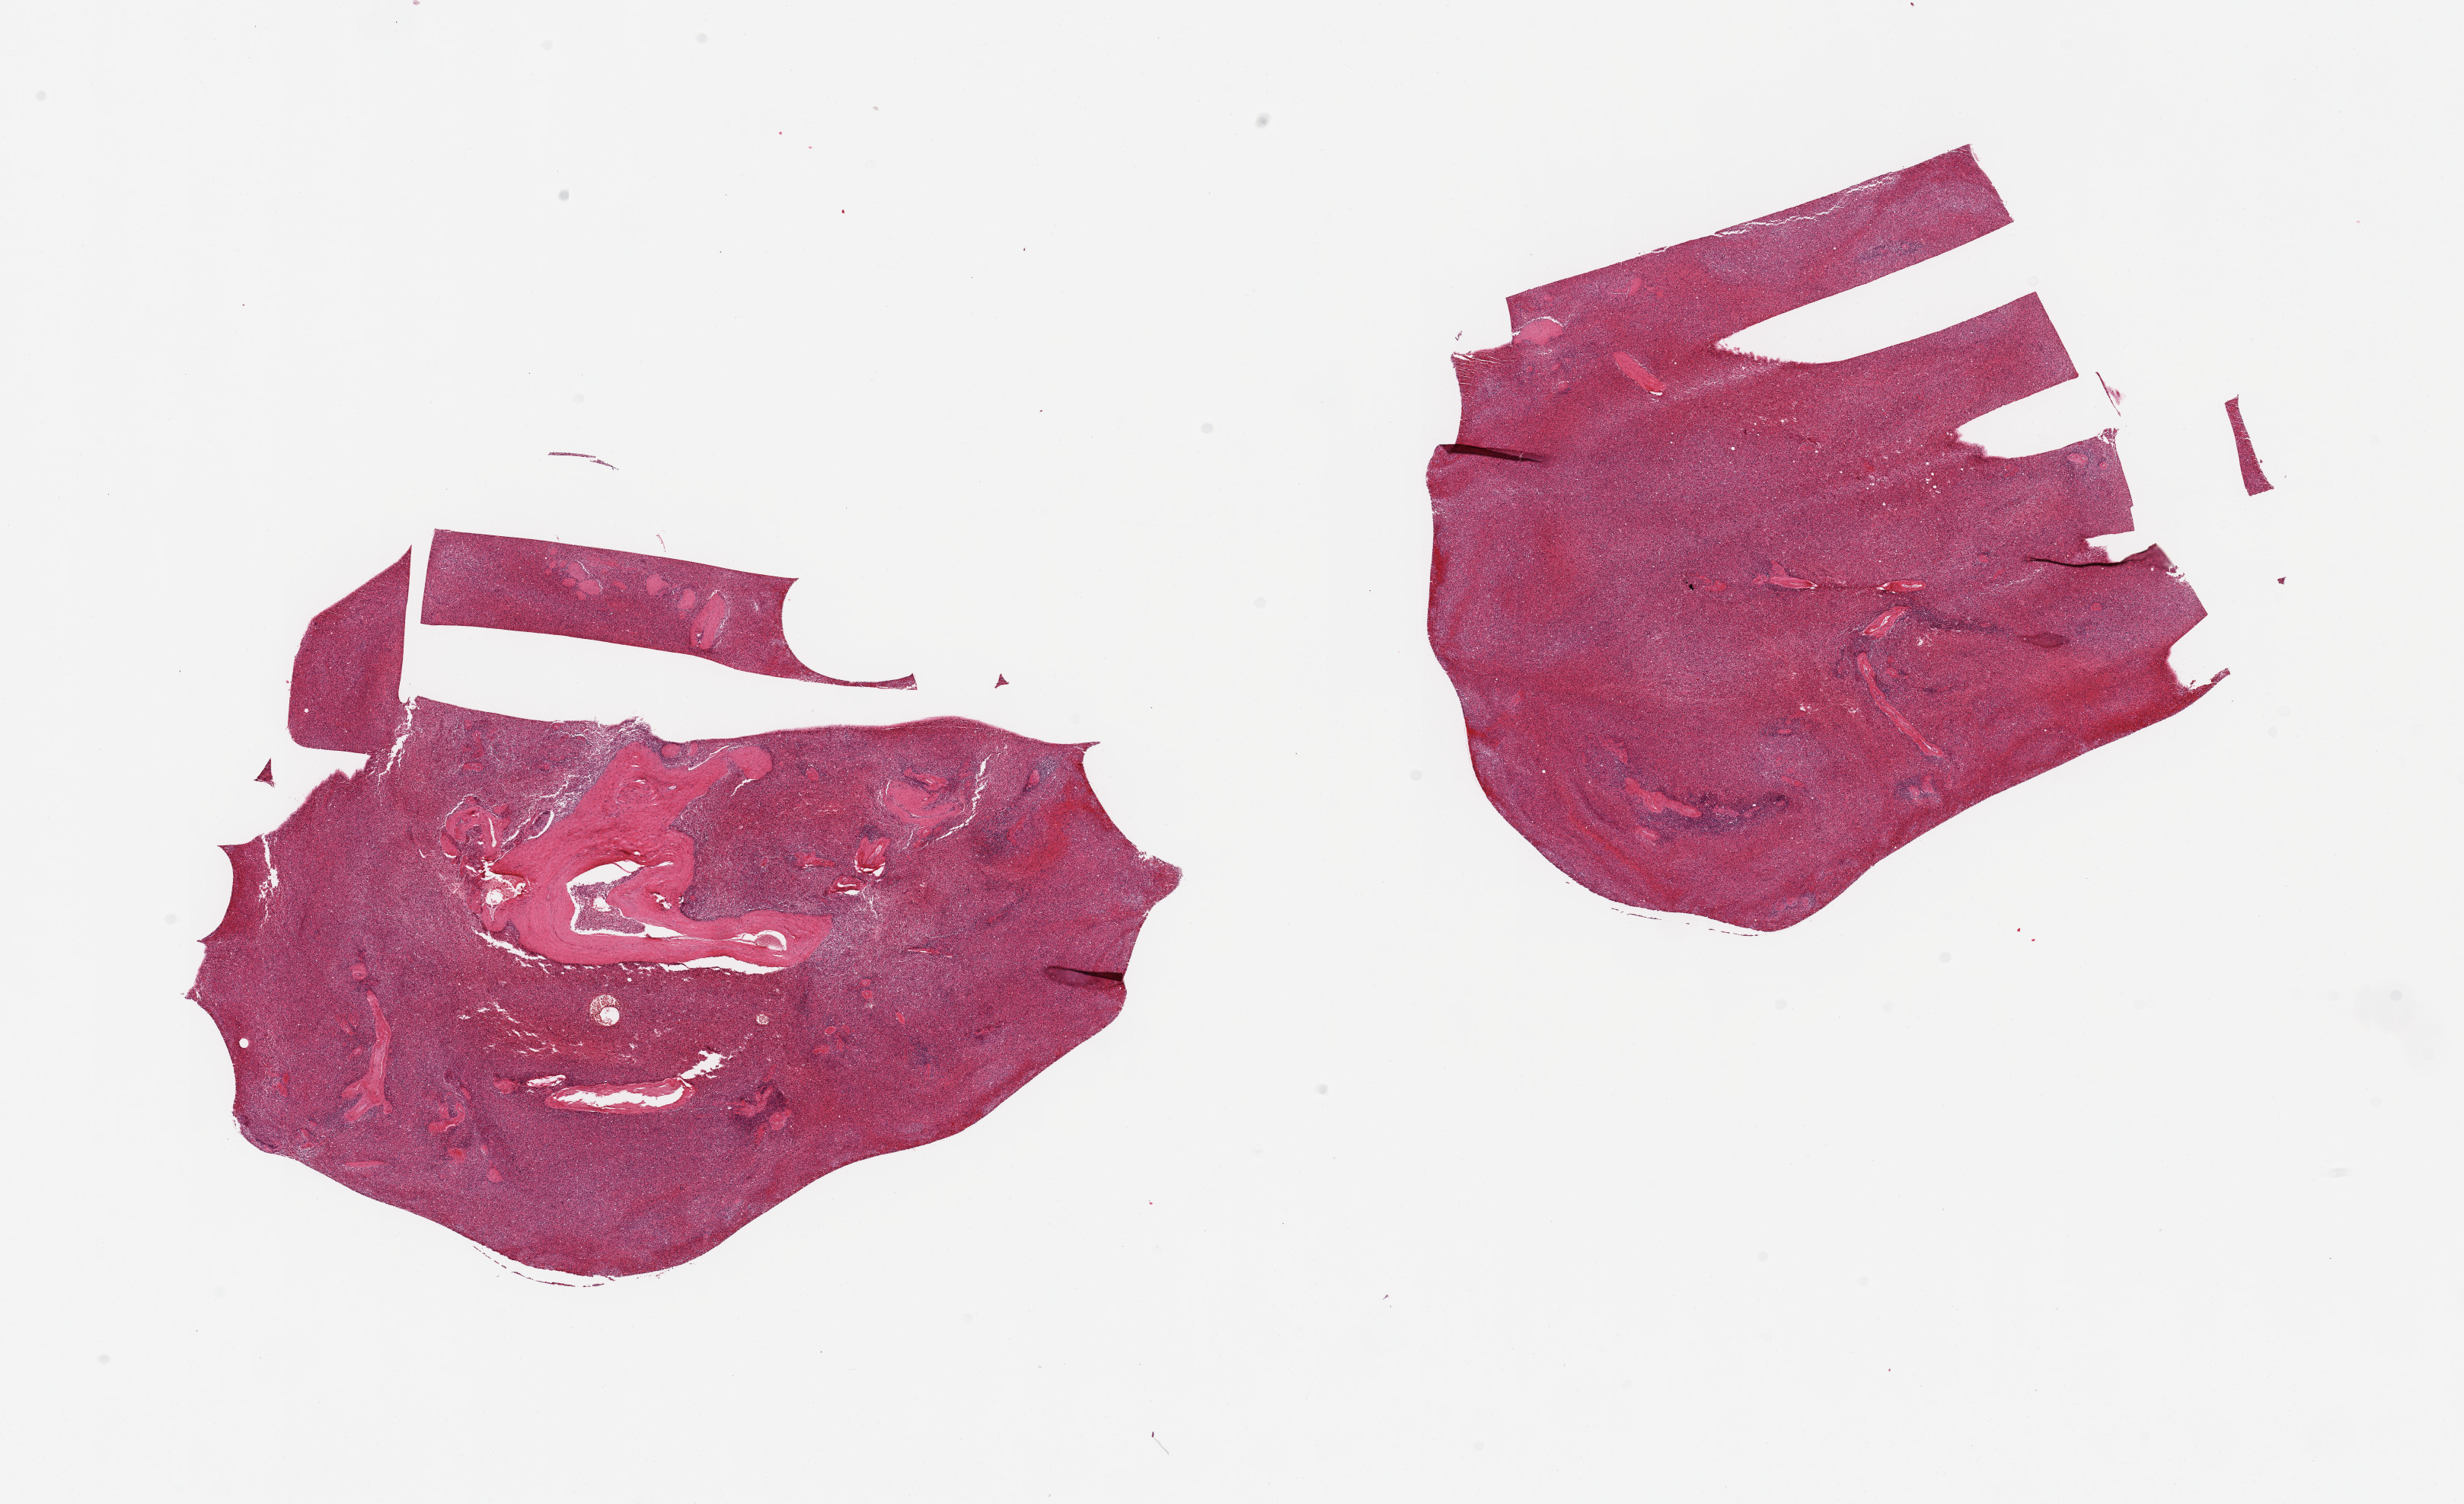
Whole-slide image, hematoxylin and eosin (H&E) stain, whole scanned area (about 25.6 x 15.6 mm) shown as a low-resolution overview. PAXgene-fixed paraffin-embedded (PFPE) section. Section of spleen (target tissue). Donor tissue sample. Male donor.
Reviewer comment on this tissue sample: 2 pieces; mild congestion.